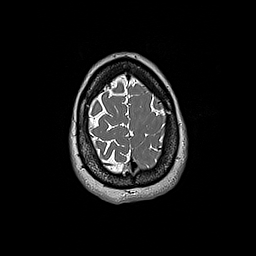
Brain MRI from a brain-tumour surgery series, one axial slice; position 46 of 192 along the scan axis; 1 mm slice thickness; 256 × 256 image matrix, field of view 250 × 250 mm. From the clinical record (not read from this slice): histopathology: Glioblastoma; WHO grade: 4; IDH mutation: no.
Outlined on this slice (expert manual segmentation):
- tumour: bounding box <160,138,166,146> (left, top, right, bottom; pixels)